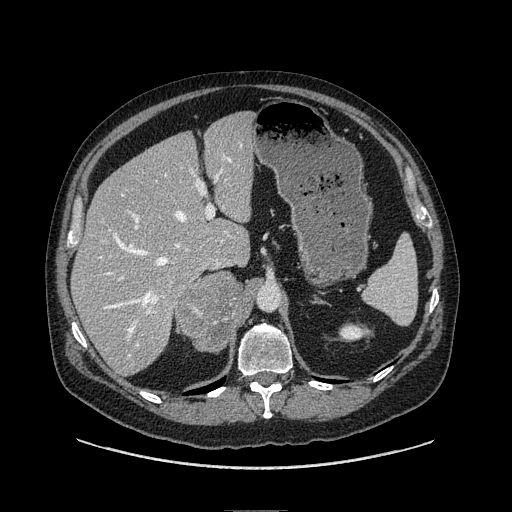
Contrast-enhanced abdominal CT, one axial slice; slice 64 of 149 in the series (ordered by position); soft-tissue window (W 400 / L 40 HU); 512 × 512 image matrix. Male patient. From the clinical record (not read from this slice): diagnosis: adrenocortical carcinoma; tumour side: right adrenal.
Structures marked on this image (semi-automatic segmentation, software-assisted and operator-edited):
- mass: bounding box [x1, y1, x2, y2] px = [177, 272, 245, 352]